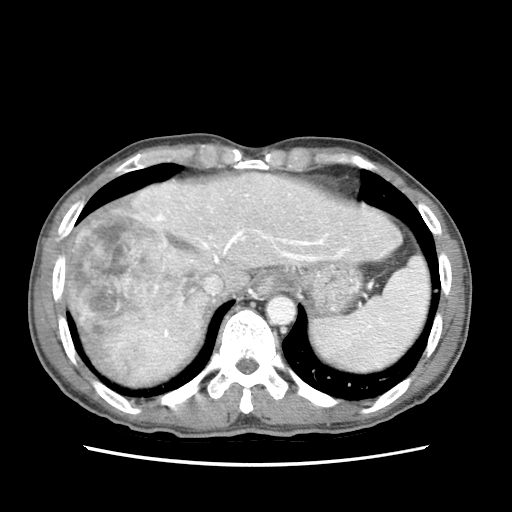
Contrast-enhanced abdominal CT (liver protocol), one axial slice. Position 60 of 79 along the scan axis. Reconstruction kernel STANDARD. 120 kVp. Soft-tissue window (W 400 / L 40 HU). 512 × 512 image matrix, field of view 320 × 320 mm. Case-level facts recorded for this patient, not image findings: diagnosis: hepatocellular carcinoma (patient treated with transarterial chemoembolisation; whether this scan precedes or follows treatment is not stated here); TNM stage (as recorded): Stage-IIIB; Child-Pugh class: A; tumour differentiation: moderately differentiated; tumour nodularity: multinodular.
Annotated regions visible in this slice (semi-automatically segmented with operator editing):
- abdominal aorta: box from (x=267, y=296) to (x=295, y=324) px
- liver parenchyma outside the tumour (the mass and vessels are separate outlines, so this box may not span the whole liver): (x=64, y=172)–(x=402, y=386)
- mass: (x=63, y=181)–(x=206, y=379)
- liver vessels: (x=158, y=189)–(x=375, y=353)